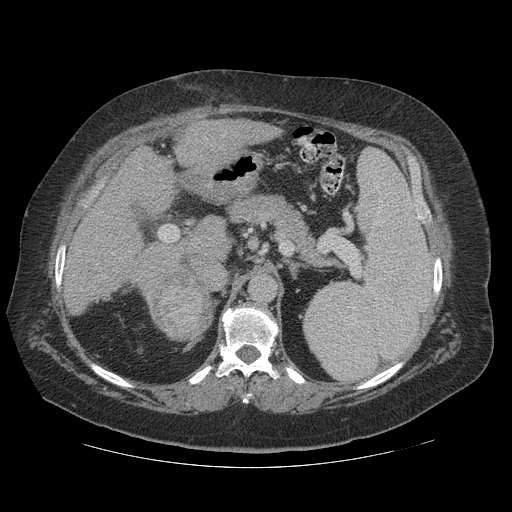
Contrast-enhanced abdominal CT (liver protocol), one axial slice. 140 kVp. Soft-tissue window (W 400 / L 40 HU). 2.5 mm slice thickness. 512 × 512 image matrix. From the clinical record (not read from this slice): diagnosis: hepatocellular carcinoma (patient treated with transarterial chemoembolisation; whether this scan precedes or follows treatment is not stated here); TNM stage (as recorded): Stage-IIIA; Child-Pugh class: A; tumour differentiation: well differentiated.
Structures marked on this image (semi-automatically segmented with operator editing):
- liver parenchyma outside the tumour (the mass and vessels are separate outlines, so this box may not span the whole liver): bounding box [x1, y1, x2, y2] px = [64, 120, 281, 316]
- mass: [149, 266, 214, 339]
- liver vessels: [81, 135, 225, 290]